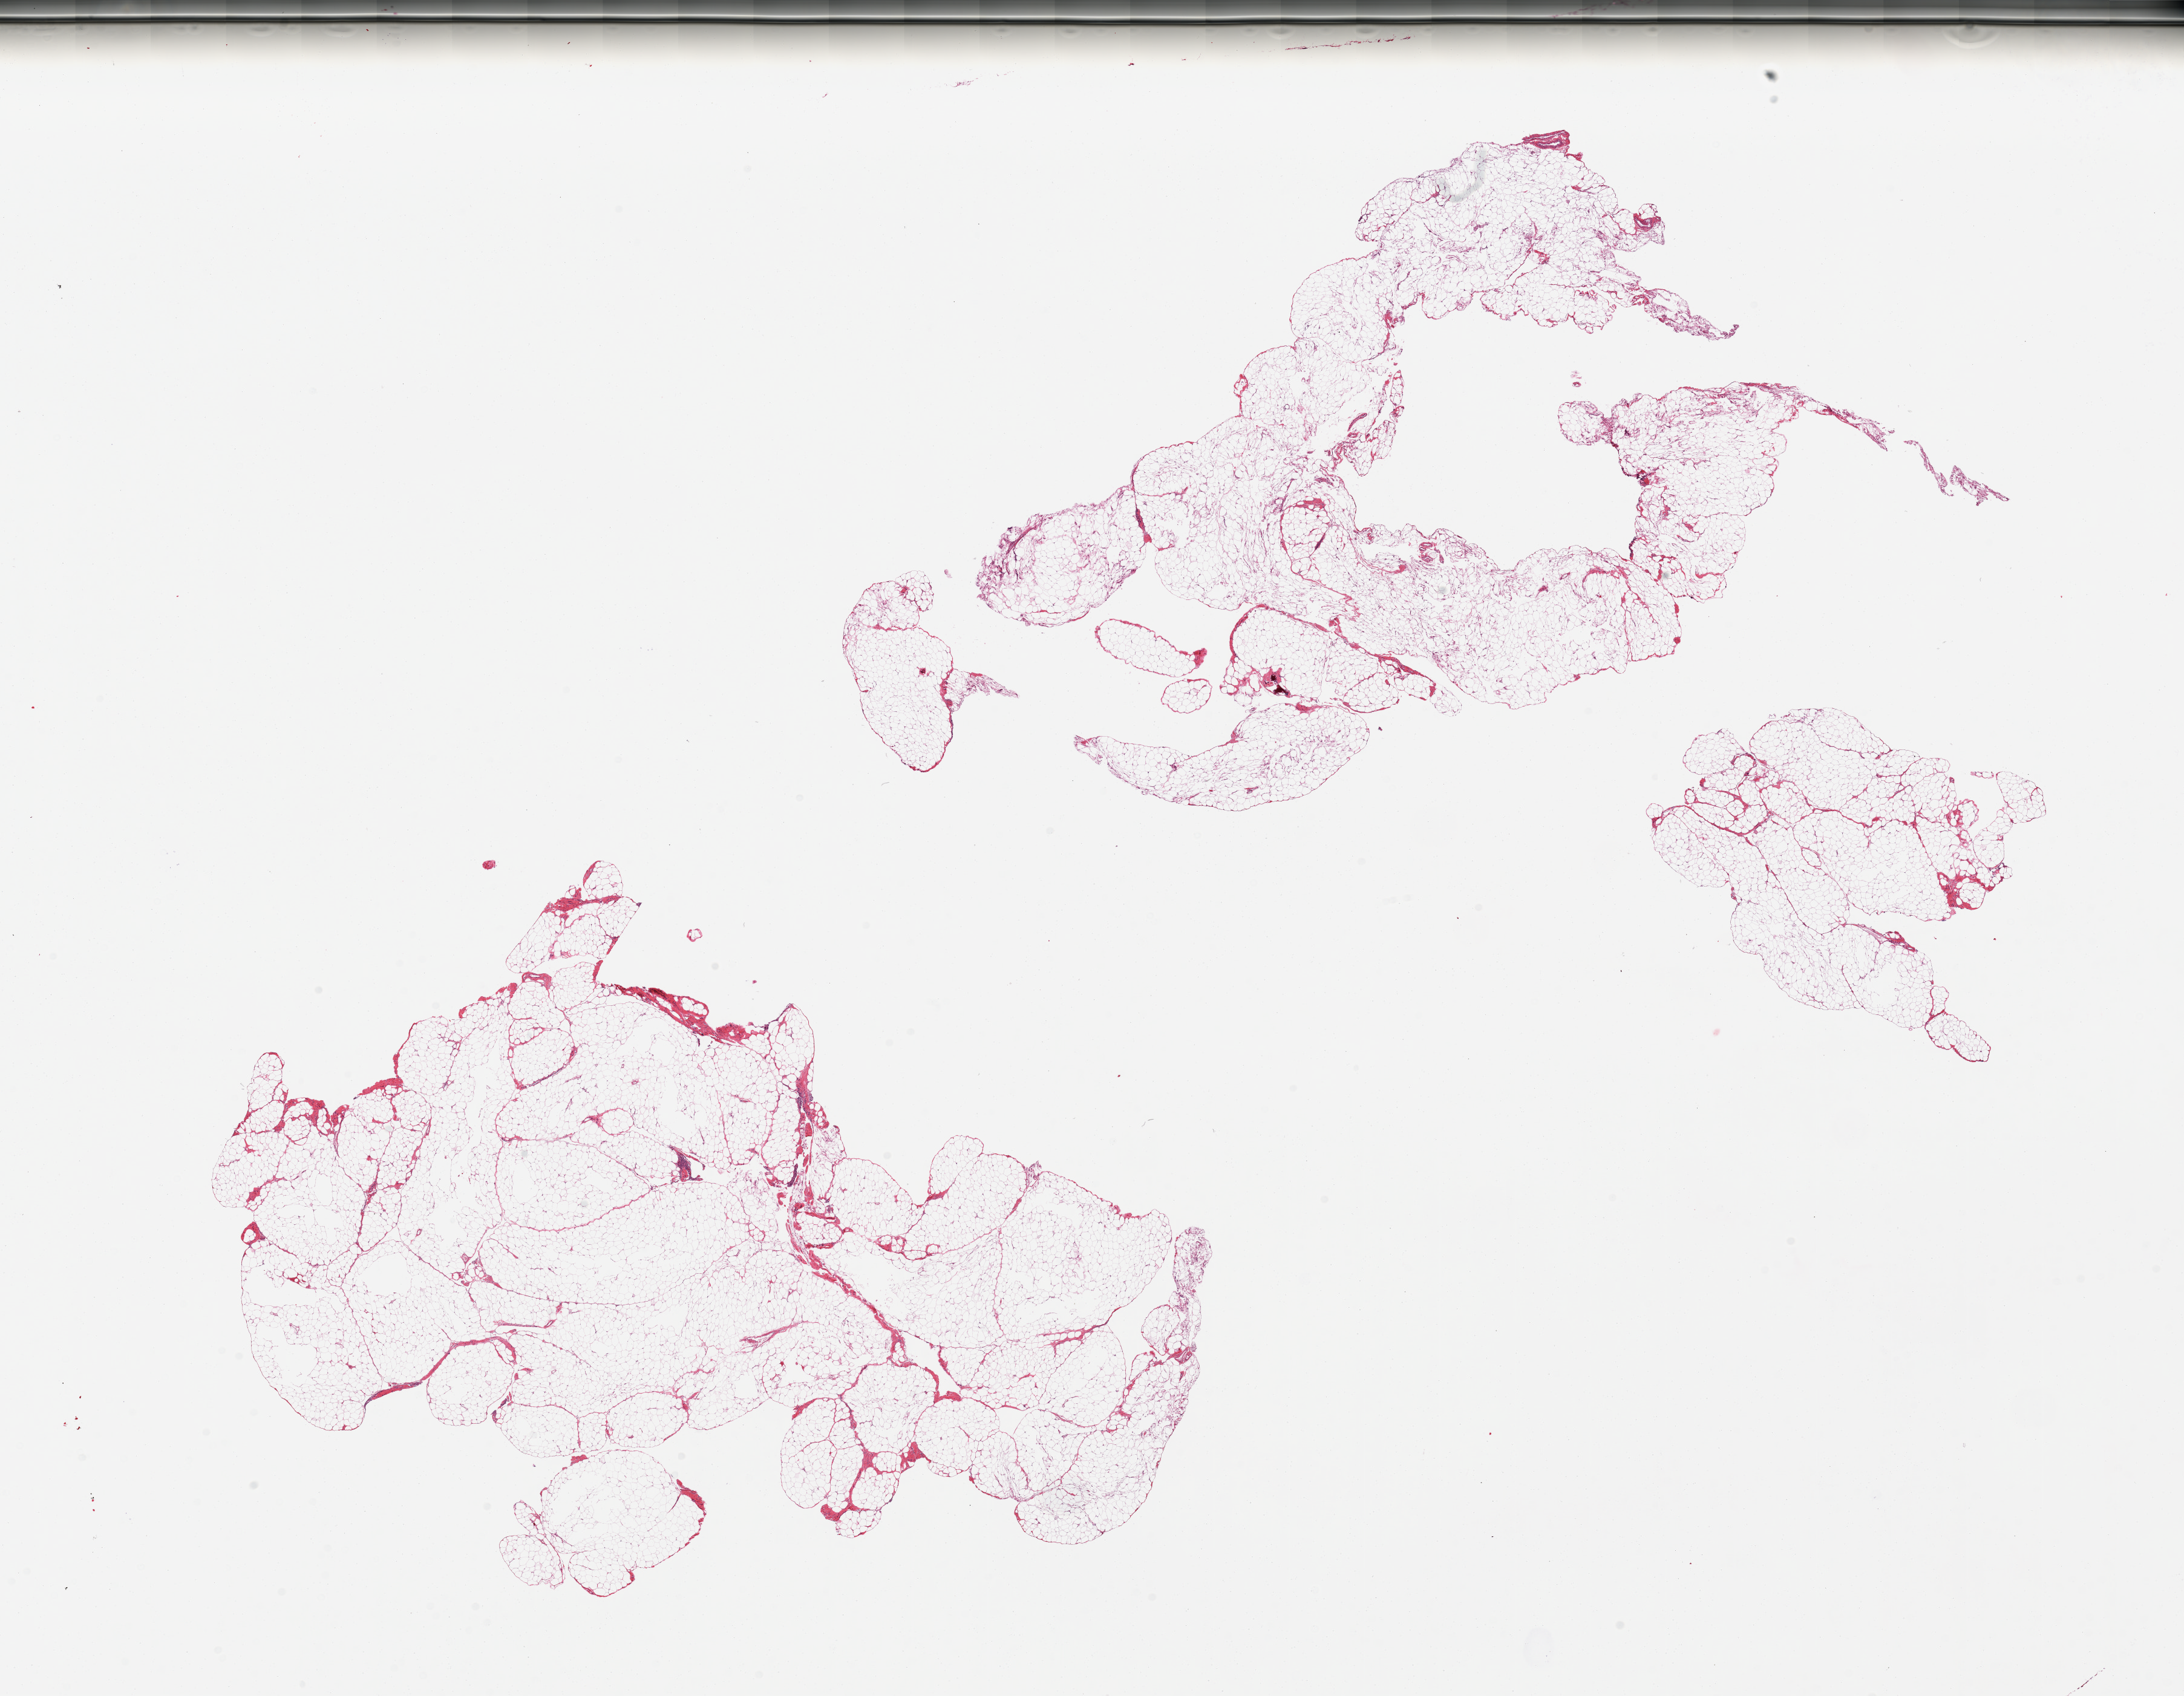
Digitized haematoxylin and eosin-stained section, brightfield — a low-resolution overview of the entire scanned area, about 28.5 x 22.2 mm, PAXgene-fixed, paraffin-embedded tissue, sampled site (target tissue): omentum, donor tissue sample. Male donor.
Pathologist's review note for this sample: 2 pieces; no abnormalities.